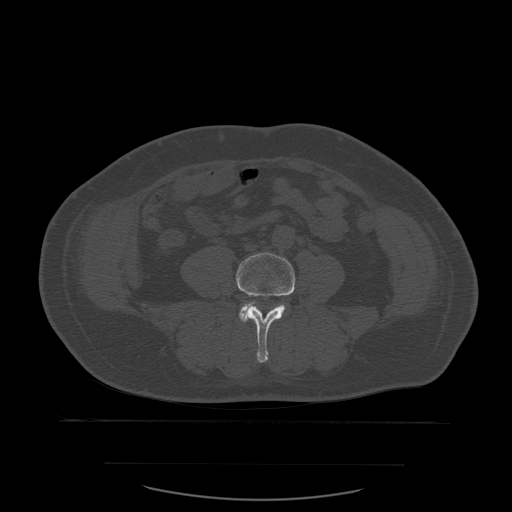
CT including the spine, one axial slice; bone window (W 1800 / L 400 HU); 1.25 mm slice thickness; 512 × 512 image matrix, field of view 479 × 479 mm. Patient age 71 years. Case-level facts recorded for this patient, not image findings: primary cancer: lung; vertebrae with lytic lesions (as recorded): T1, T2, L5, S1.
Outlined on this slice (semi-automatic segmentation, software-assisted and operator-edited):
- L4 vertebra: box from (x=236, y=253) to (x=296, y=363) px
- L5 vertebra: (x=240, y=302)–(x=283, y=320)